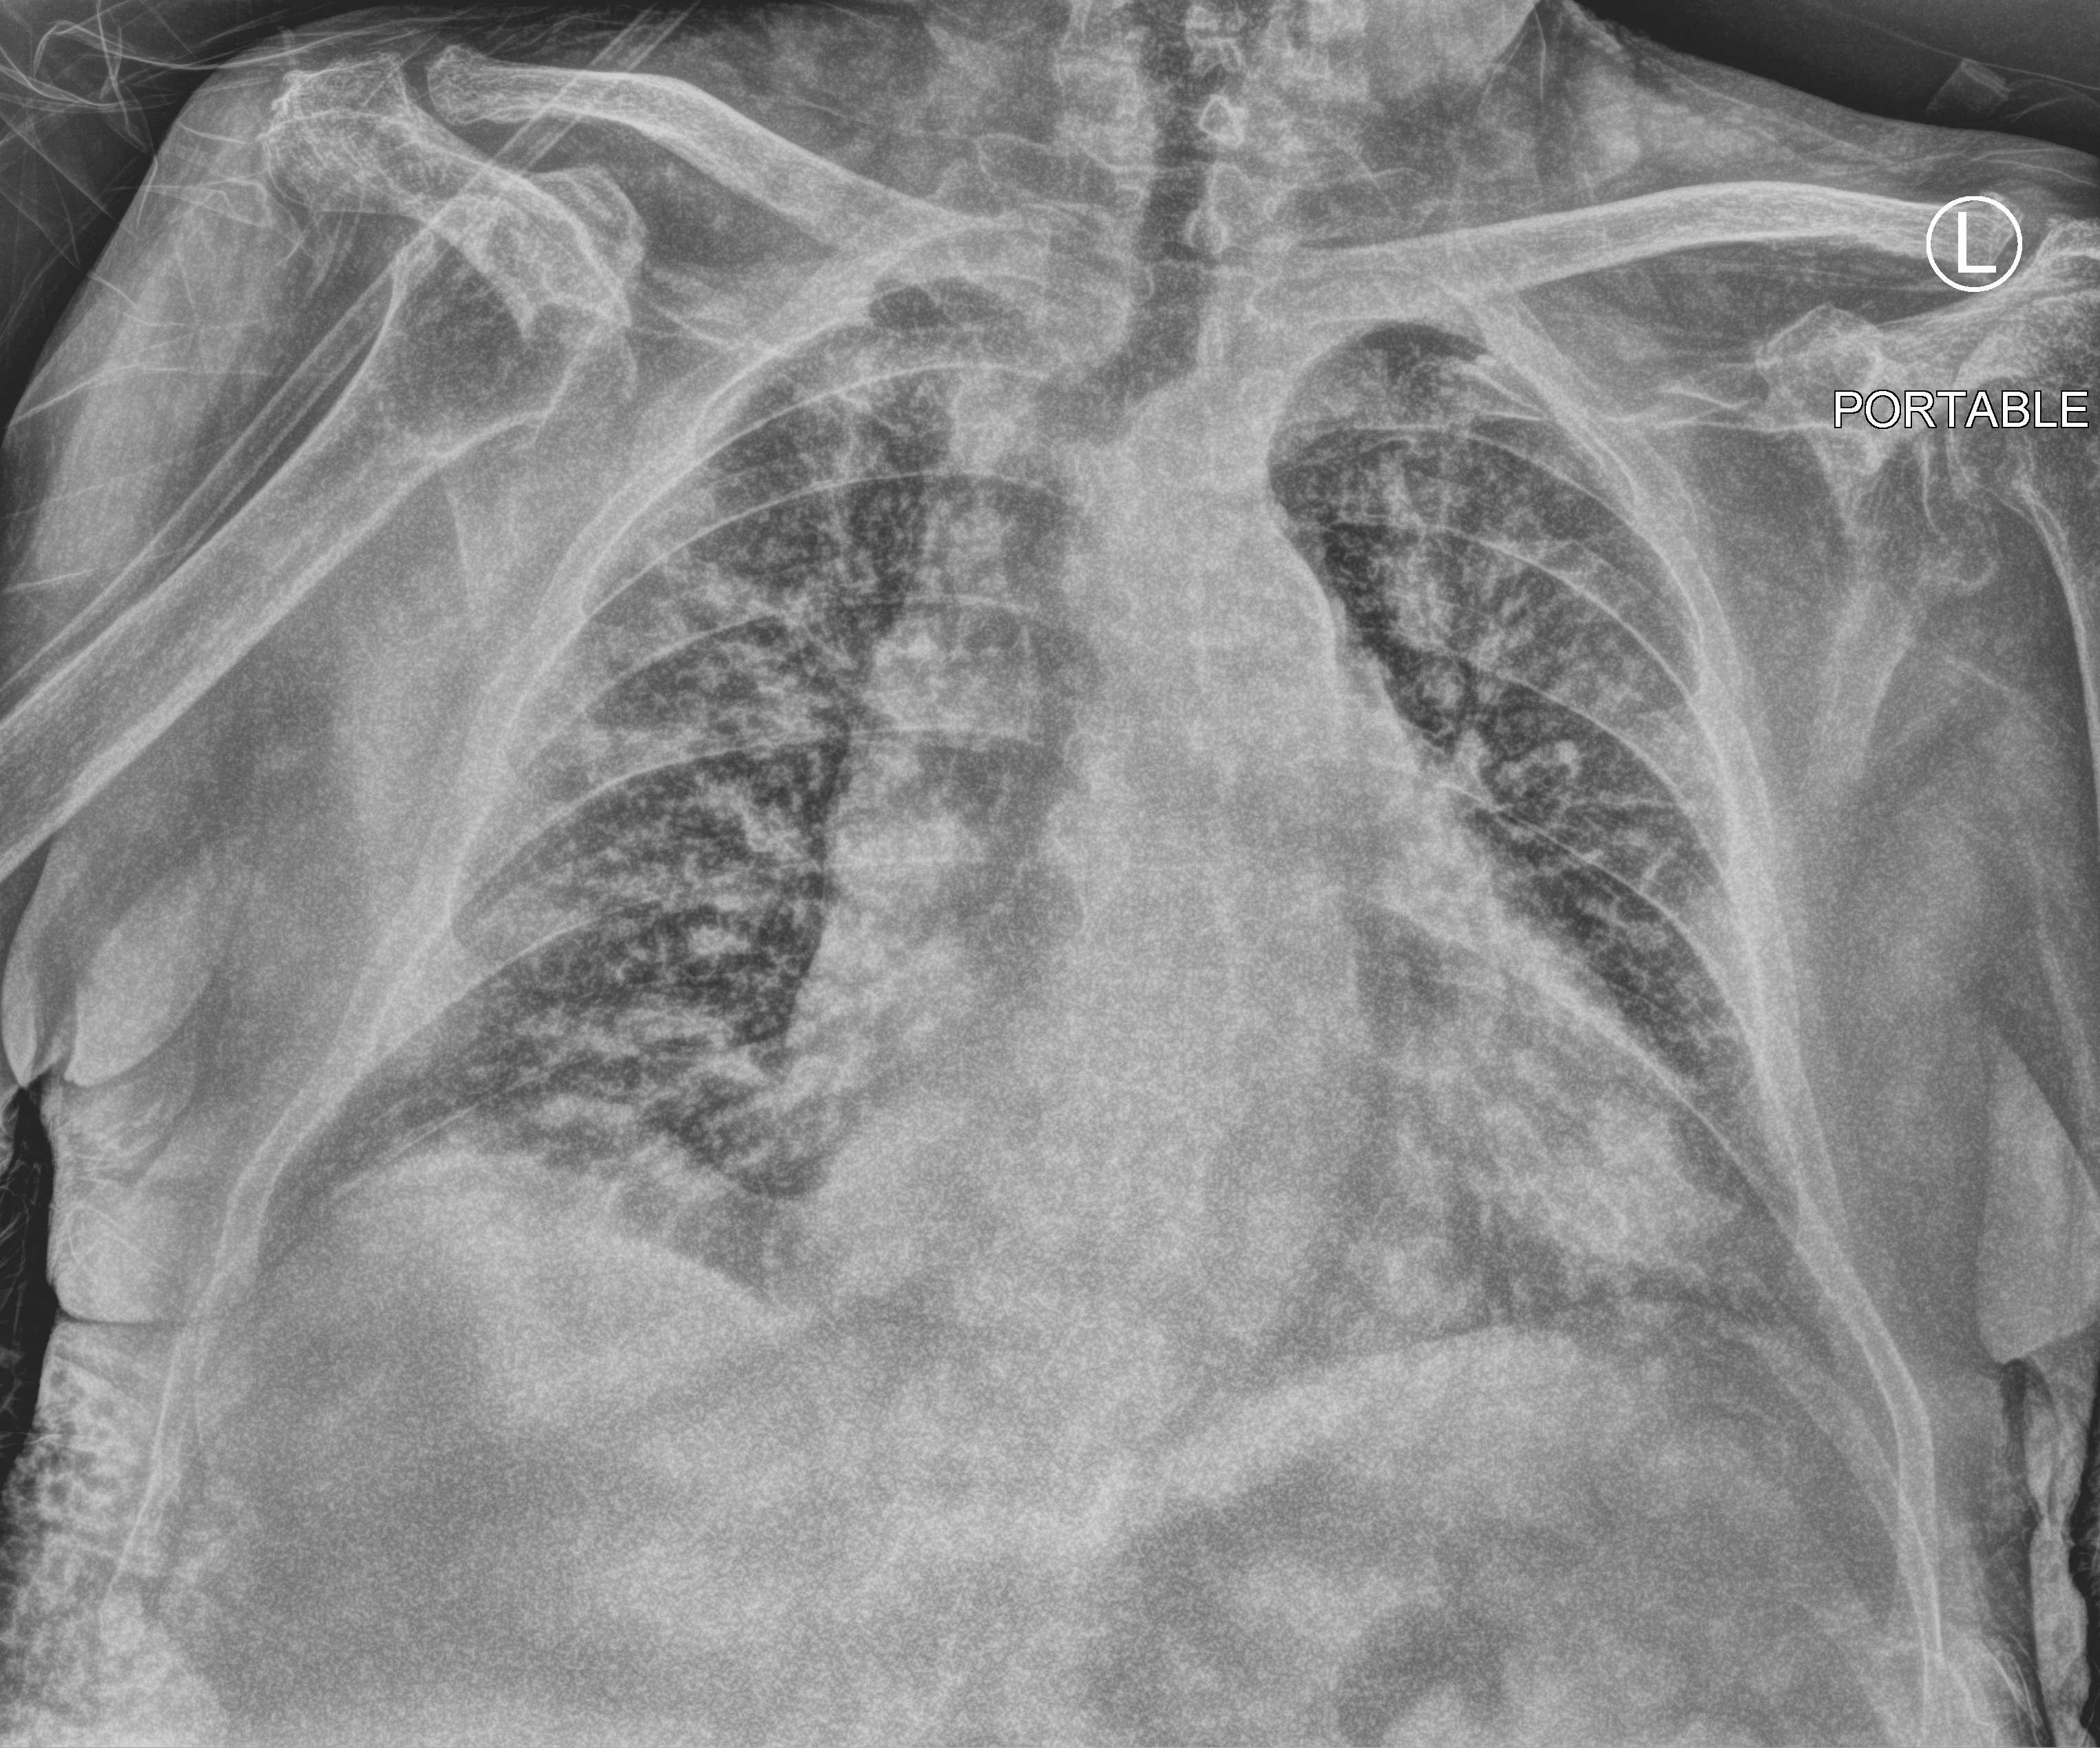
Portable chest radiograph; anteroposterior (AP) projection. Male patient hospitalised with COVID-19, age 75–90 years.
Admission-level facts for this patient (not findings on this image; timing relative to this image not recorded):
- hypertension (admission record): yes
- smoking status (admission record): former
- admitted to intensive care during this hospital stay: no